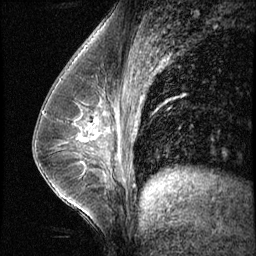
Breast MRI (dynamic contrast-enhanced), one sagittal slice; position 34 of 60 along the scan axis; 3 images stored at this slice position (order not interpretable as contrast timing); 1.5 T; TE 4.2 ms, TR 8.7 ms; 2.5 mm slice thickness; 256 × 256 image matrix. Patient: female, 35 years. Case-level facts recorded for this patient, not image findings: setting: breast cancer imaged before/during neoadjuvant chemotherapy; receptor status: HER2-positive.
Structures marked on this image (semi-automatic segmentation, software-assisted and operator-edited):
- analysis volume of interest (the breast-tissue region the enhancement analysis was run in; not a lesion): box from (x=65, y=102) to (x=121, y=156) px
- tumour enhancement mask (voxels above the 140 % enhancement threshold inside the analysis volume of interest): (x=74, y=118)–(x=96, y=131)